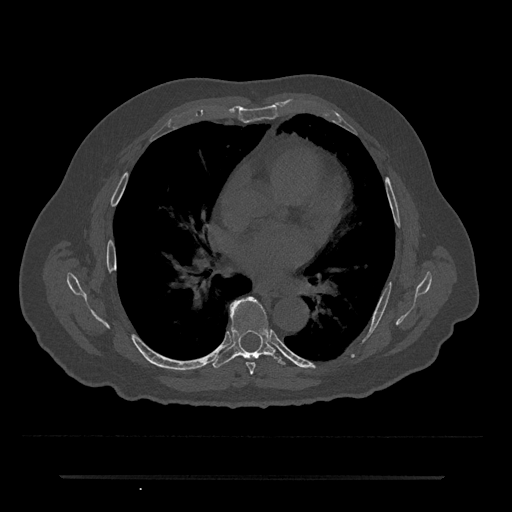
CT including the spine, one axial slice. Position 403 of 797 along the scan axis. 120 kVp. Bone window (W 1800 / L 400 HU). 0.5 mm slice thickness. 512 × 512 image matrix, field of view 437 × 437 mm. Patient: male, 69 years. From the clinical record (not read from this slice): primary cancer: prostate.
Outlined on this slice (semi-automatically segmented with operator editing):
- T6 vertebra: bounding box <246,362,255,375> (left, top, right, bottom; pixels)
- T7 vertebra: <212,297,285,368>